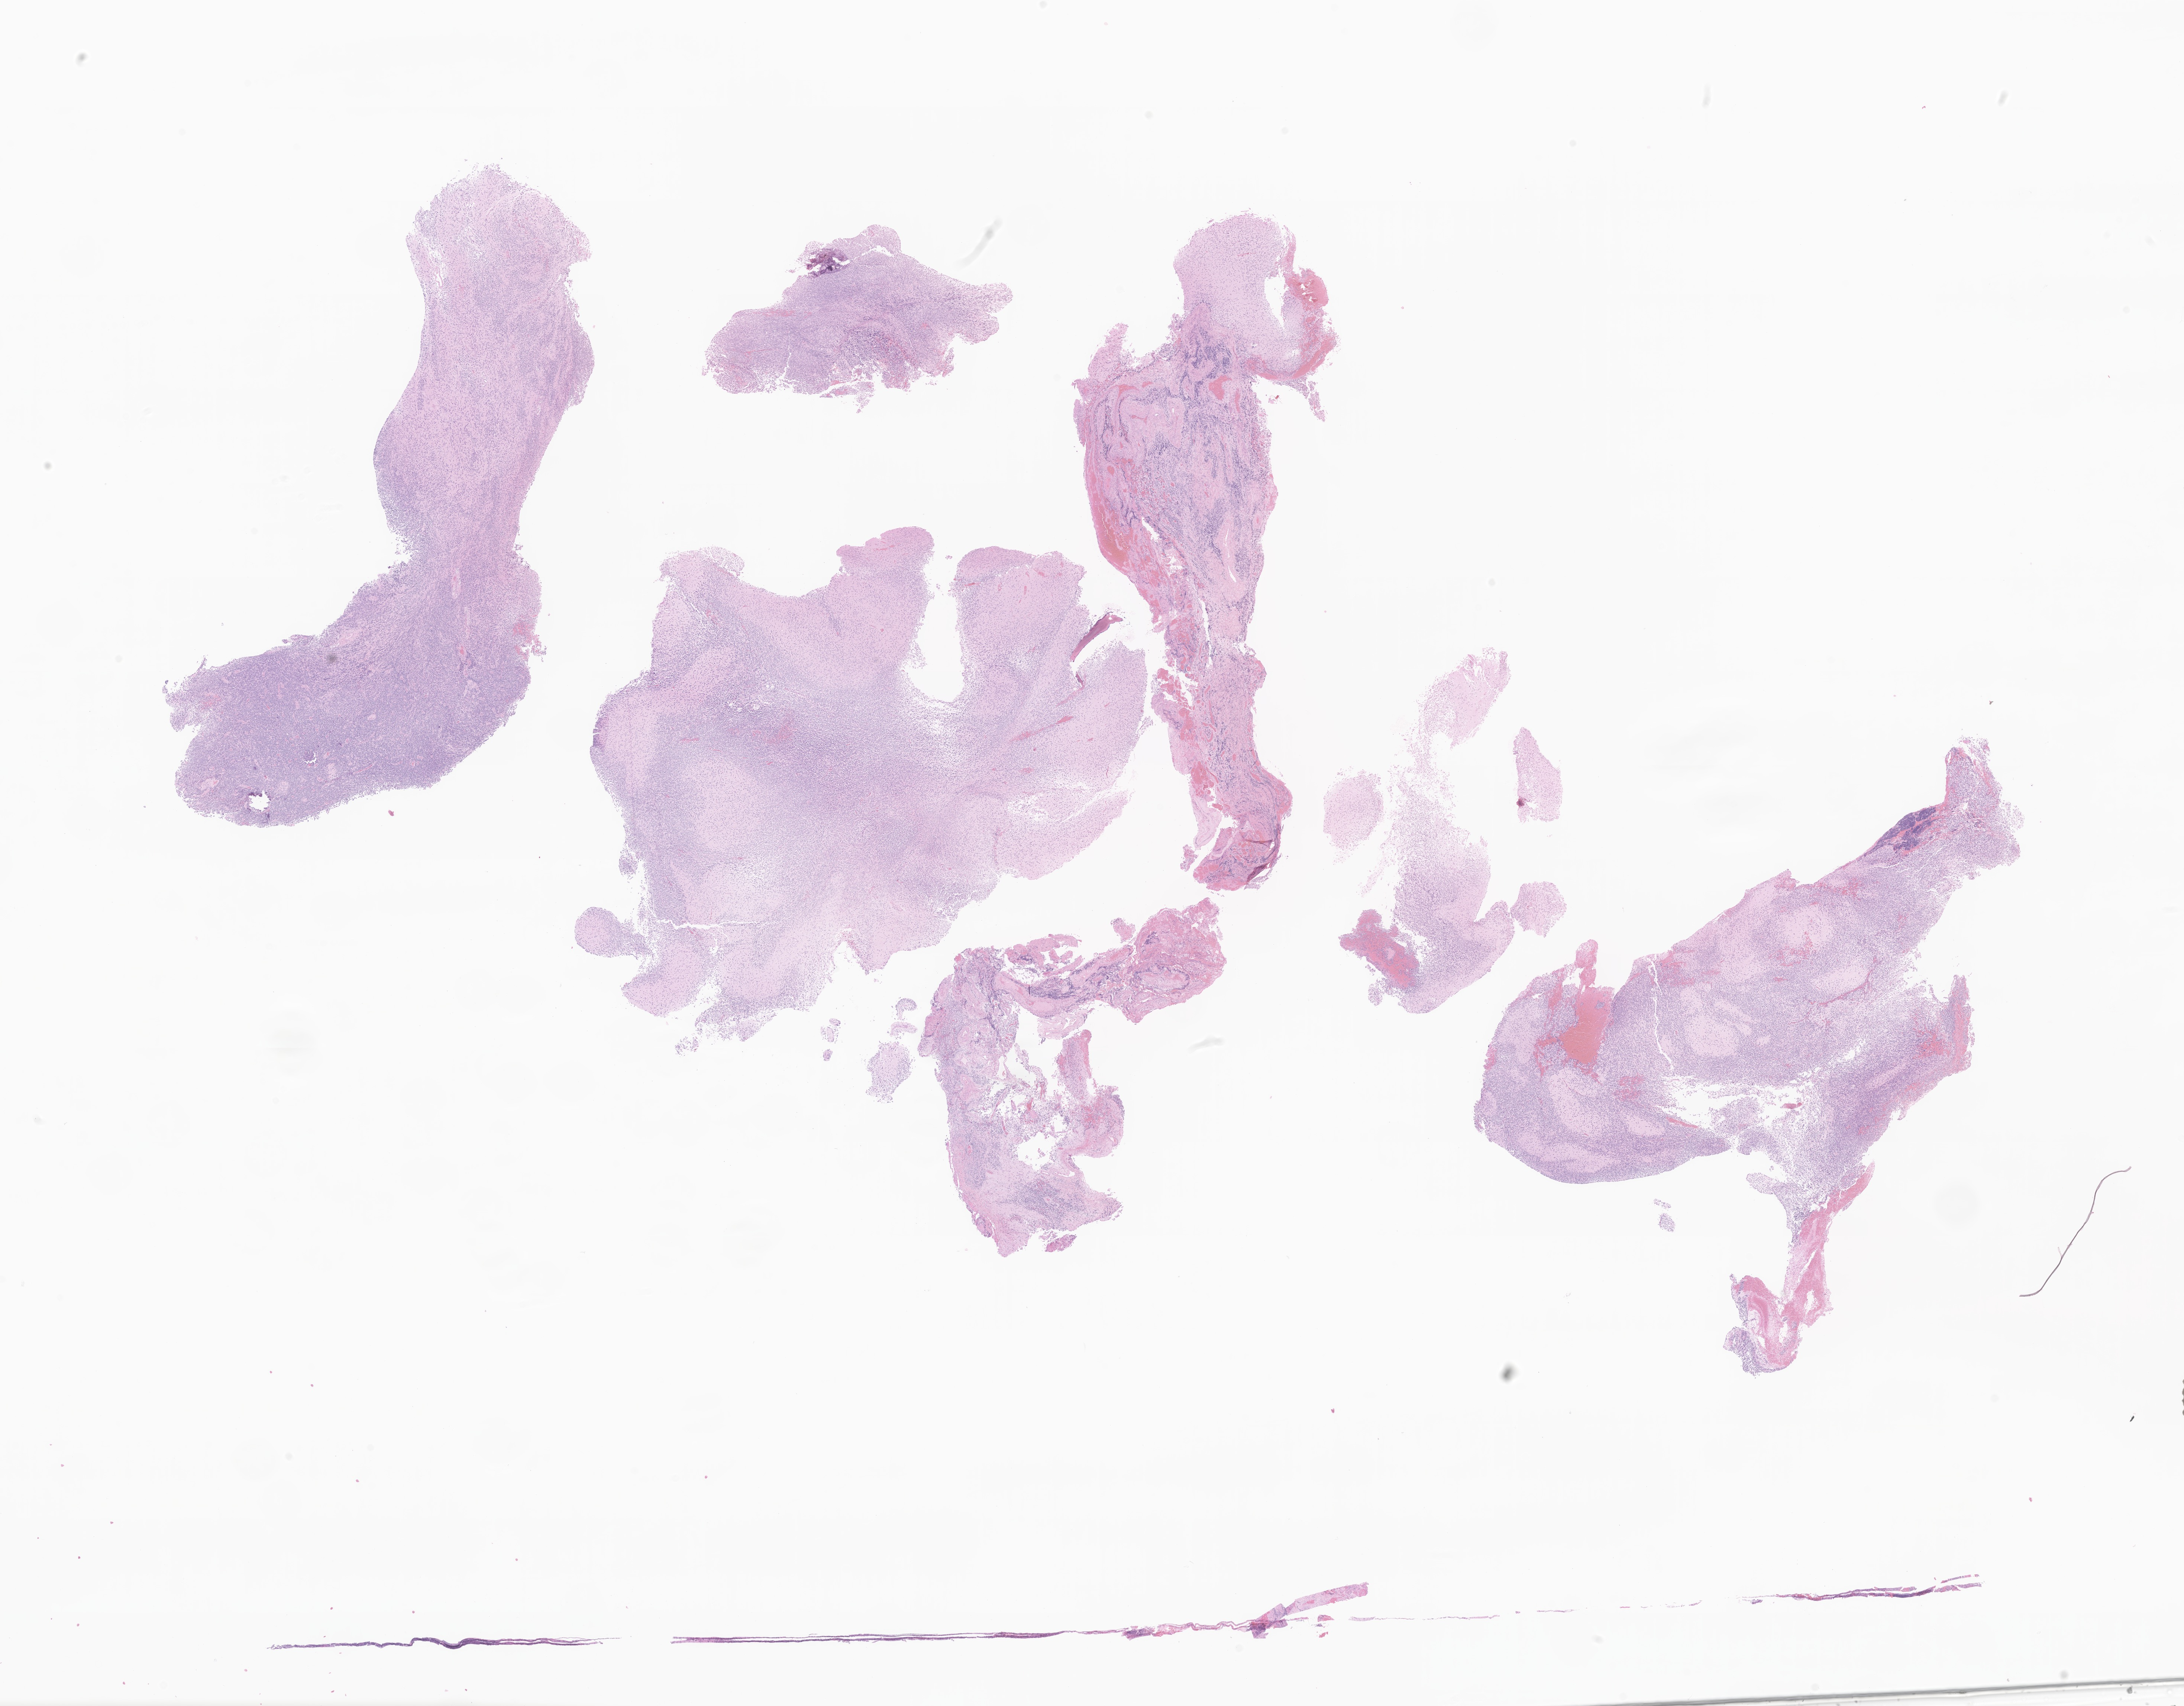
Haematoxylin and eosin whole-slide image of tumor tissue from the cerebellum — shown as a low-resolution overview of the whole scanned area (about 24.8 x 19.3 mm), formalin-fixed, paraffin-embedded (FFPE) tissue. Patient male; age 93 months (7 years 9 months).
* recorded diagnosis: Medulloblastoma, NOS